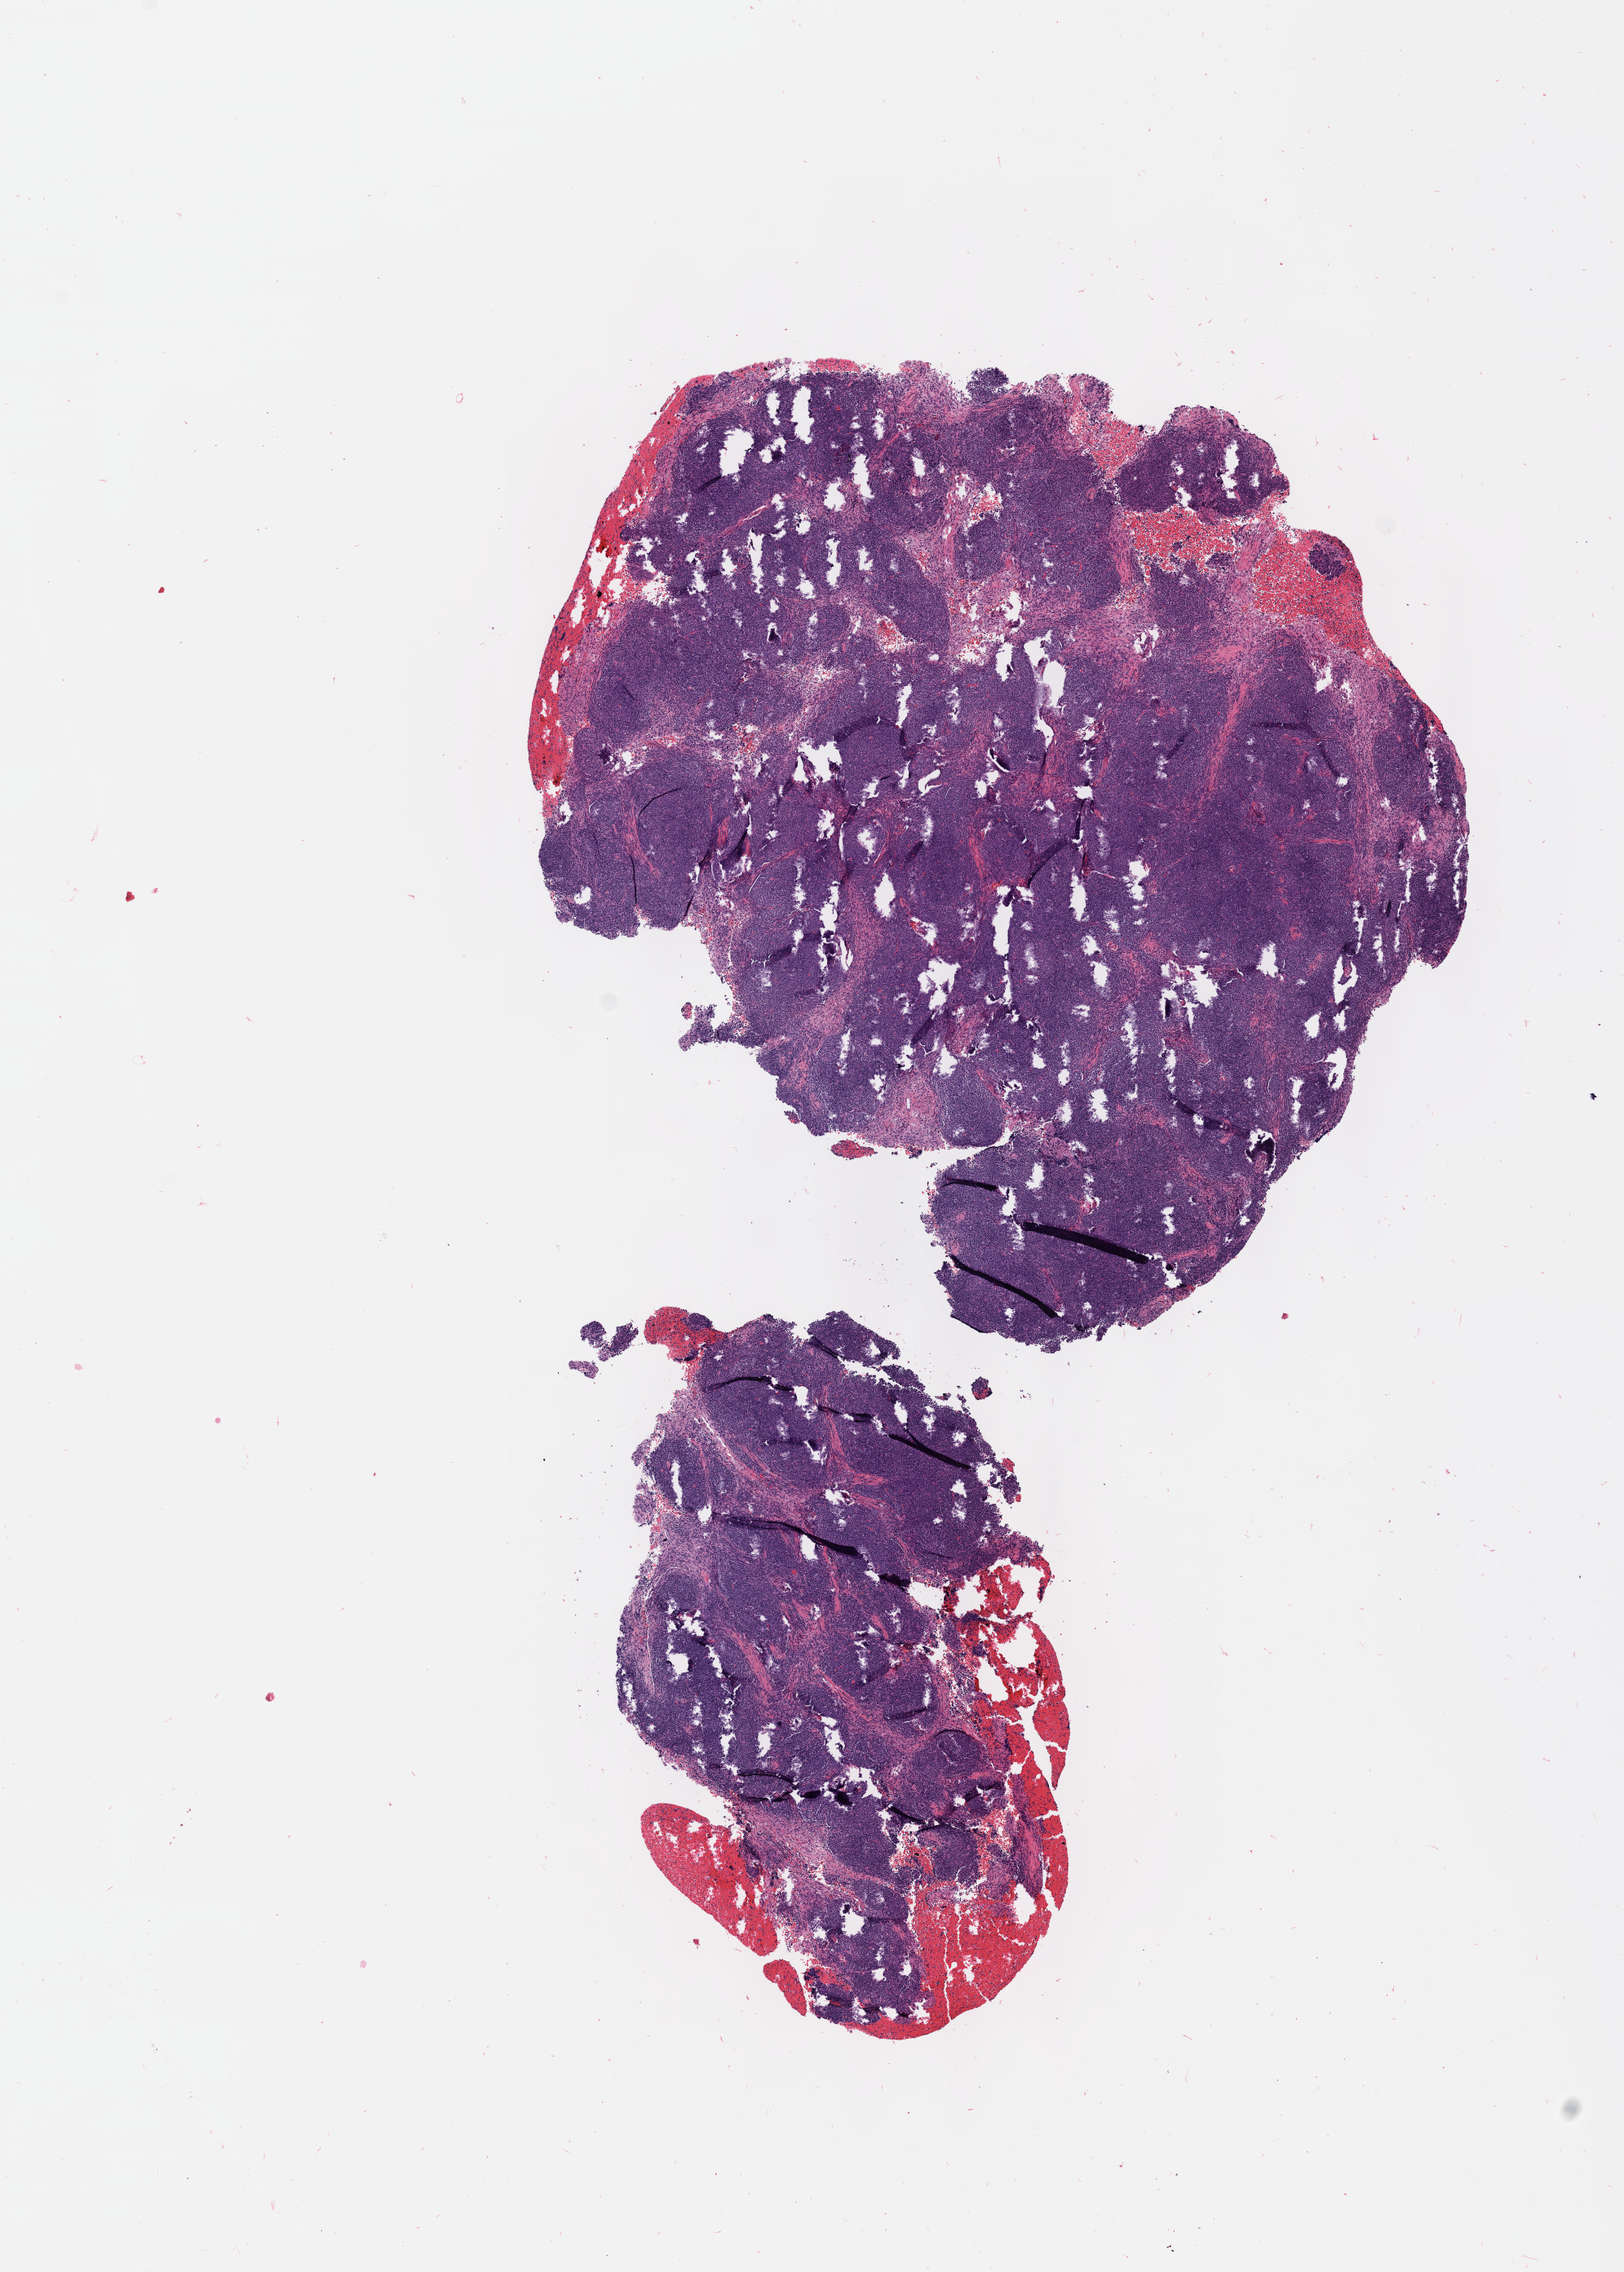
H&E-stained whole-slide image, low-resolution overview of the scanned area, about 8.1 x 11.3 mm. Formalin-fixed paraffin-embedded (FFPE) diagnostic section. Primary tumour sample from the thymus. Patient: male, age at initial diagnosis 68 years.
Diagnosis: Thymoma, type AB, NOS.